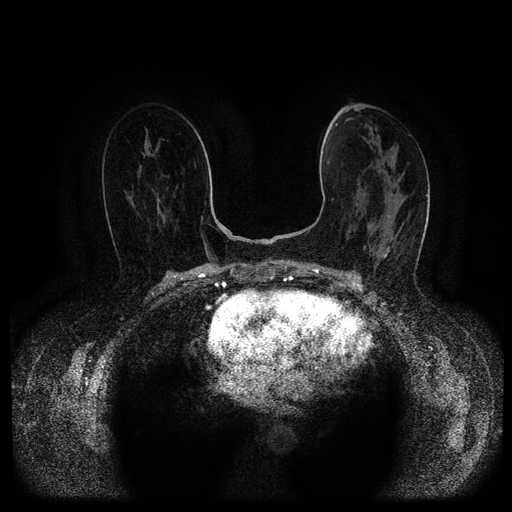
Breast MRI (dynamic contrast-enhanced, multi-phase), one axial slice; slice 55 of 116 in the series (ordered by position); dynamic contrast-enhanced series, time point 2 of 5 at this slice position (early post-contrast); 1.5 T; TE 2.6 ms, TR 5.4 ms; 2 mm slice thickness; 512 × 512 image matrix, field of view 340 × 340 mm. Patient: female, 61 years.
Structures marked on this image (semi-automatically segmented with operator editing):
- breast lesion (labelled 'tumour' in the annotation; benign lesions carry a separate 'benign' label): bounding box [x1, y1, x2, y2] px = [382, 253, 388, 259]